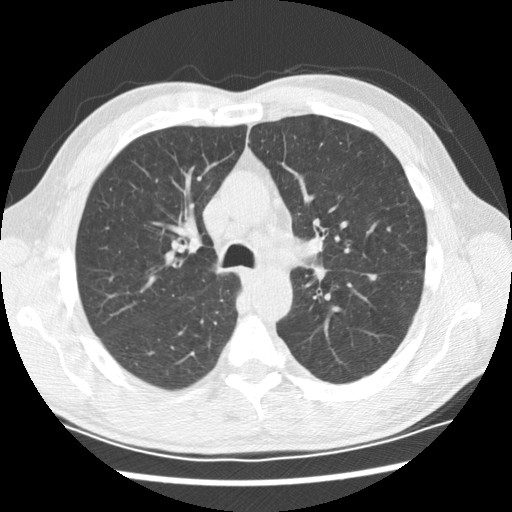
Low-dose screening chest CT, one axial slice; slice 135 of 208 in the series (ordered by position); 120 kVp; lung window (W 1500 / L -600 HU); 2.5 mm slice thickness; 512 × 512 image matrix, field of view 340 × 340 mm.
Outlined on this slice (outlined manually by an expert reader):
- lesion 2 (tumor, lower lobe of left lung): bounding box (x1, y1, x2, y2) in pixels: (368, 274, 377, 282)